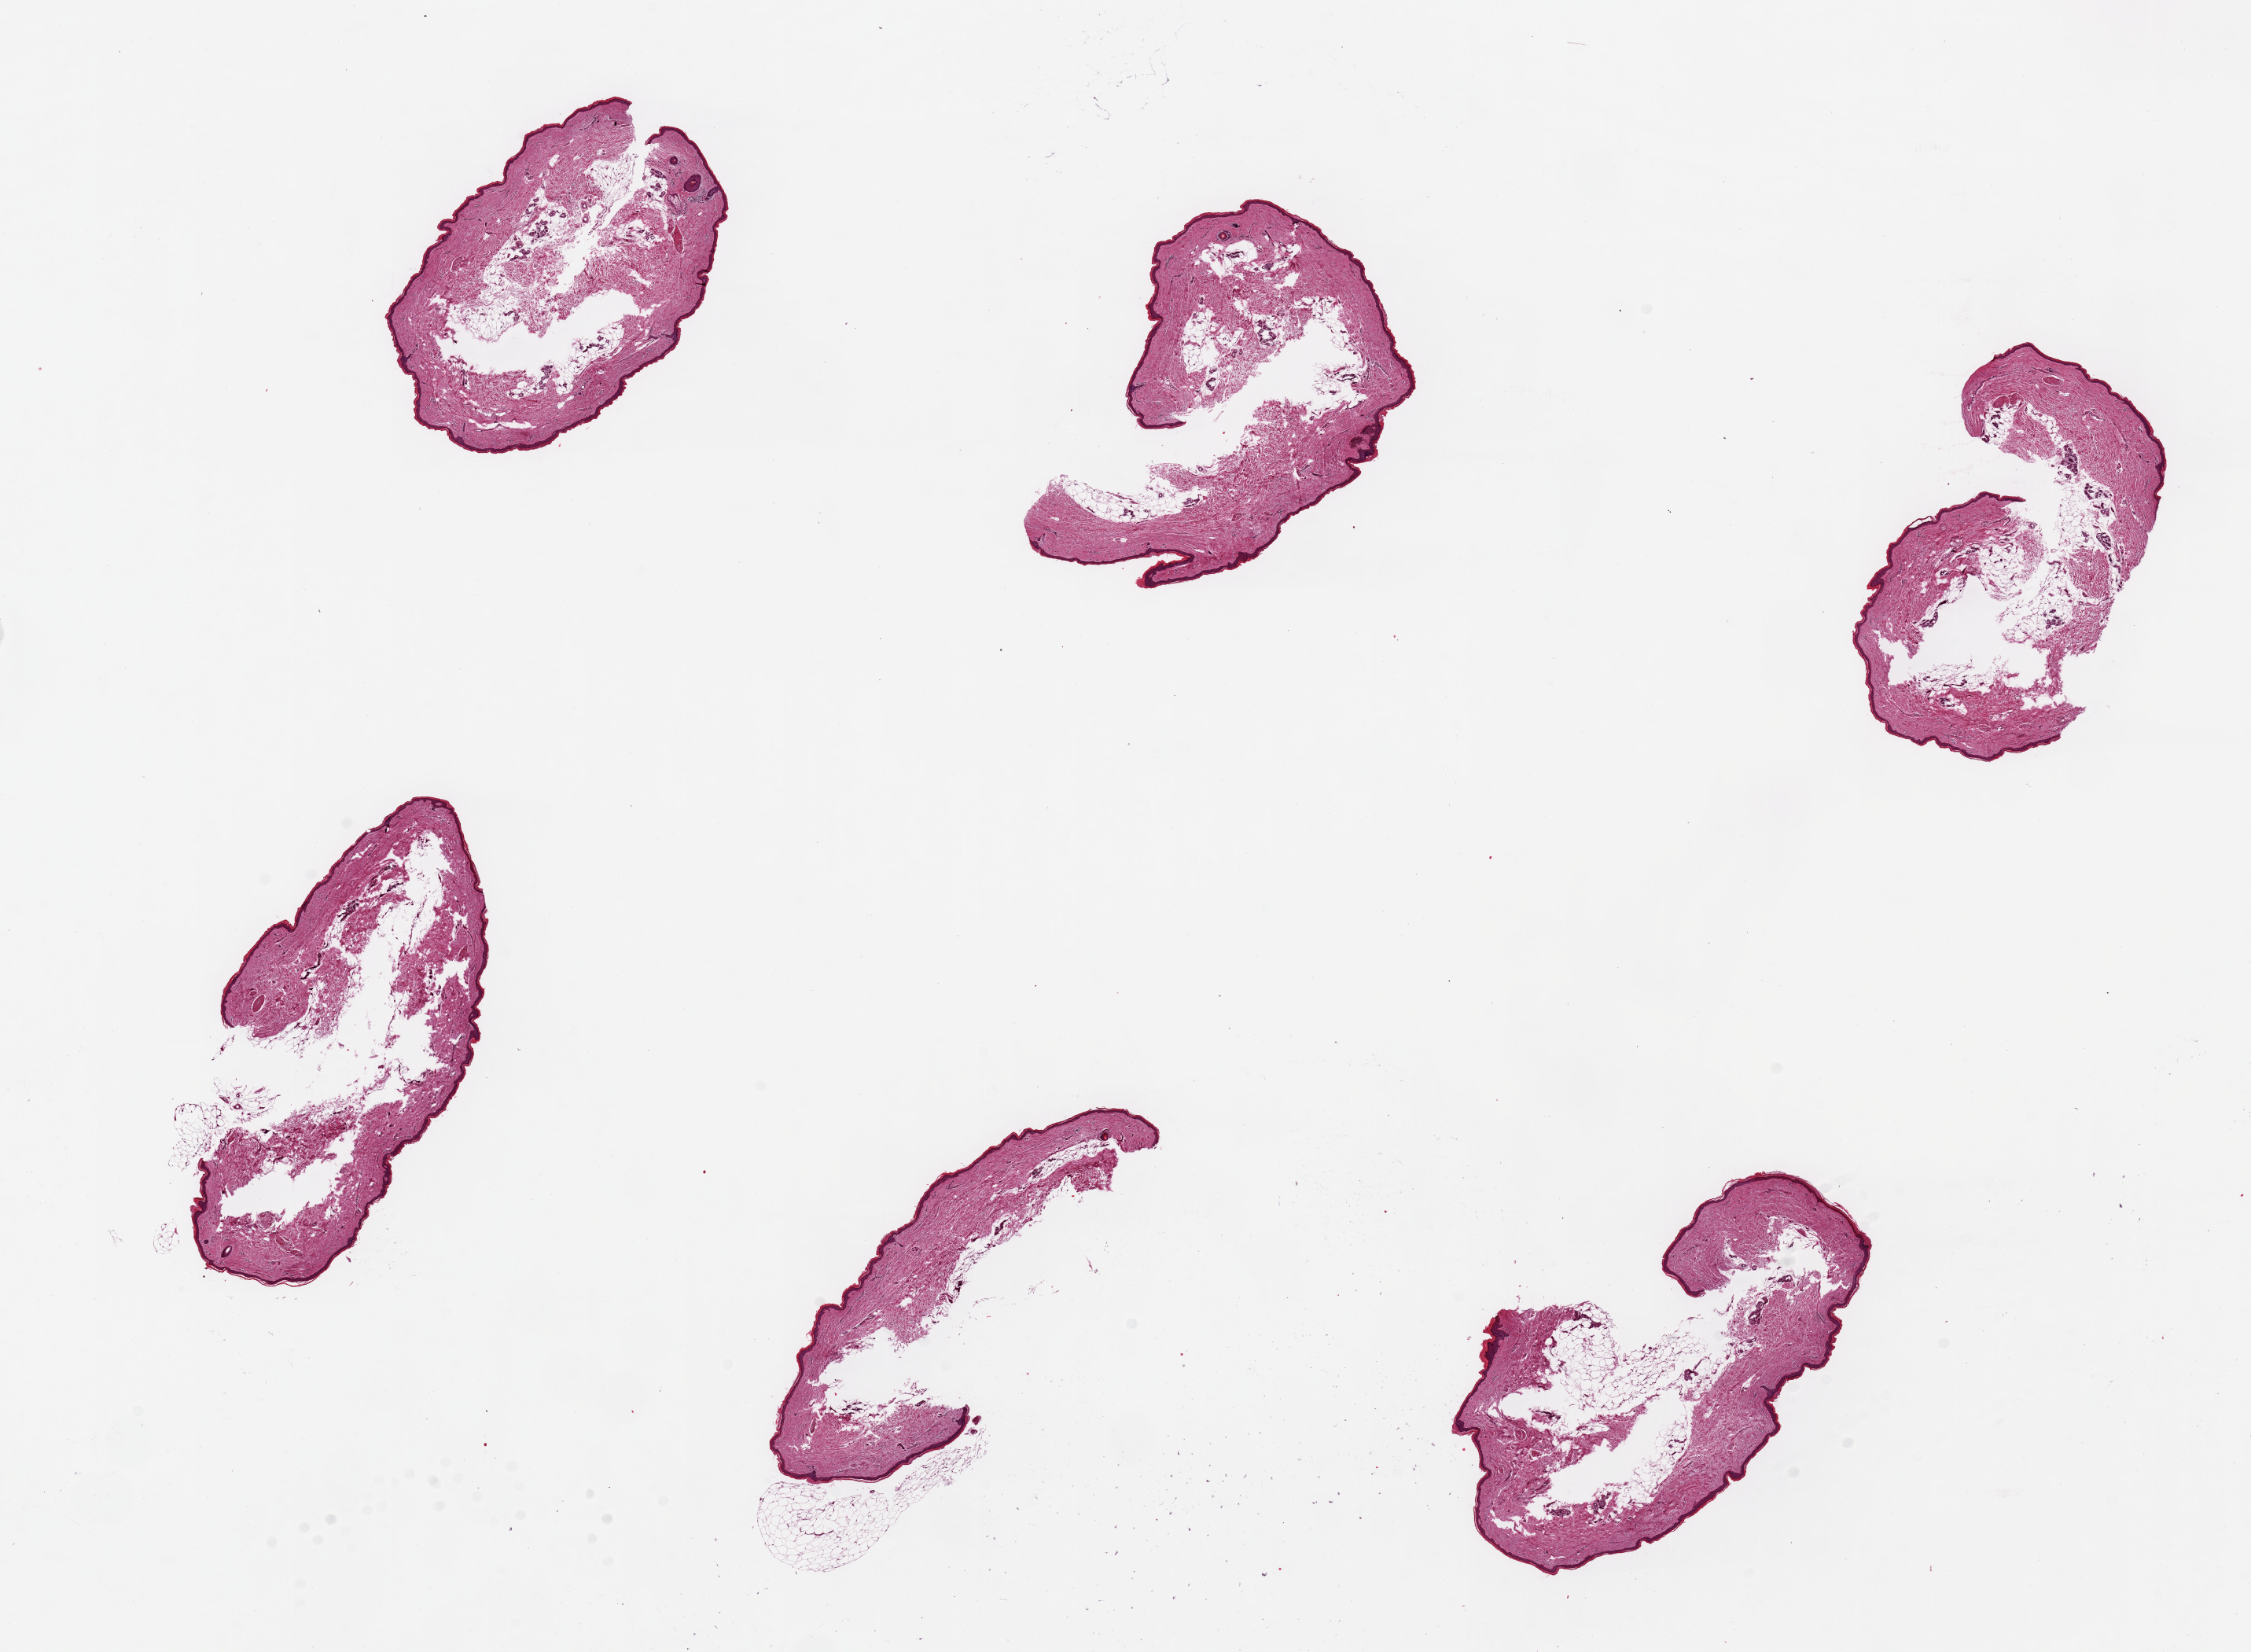
Hematoxylin and eosin (H&E) whole-slide image — low-resolution overview of the scanned area, about 22.6 x 16.6 mm (from a 20x scan); PAXgene-fixed, paraffin-embedded tissue; section of skin of lower leg (target tissue); tissue donor sample. Female donor.
* pathologist's review note for this sample: 6 pieces, up to 5x2mm; squamous epithelium is ~2-3% thickness